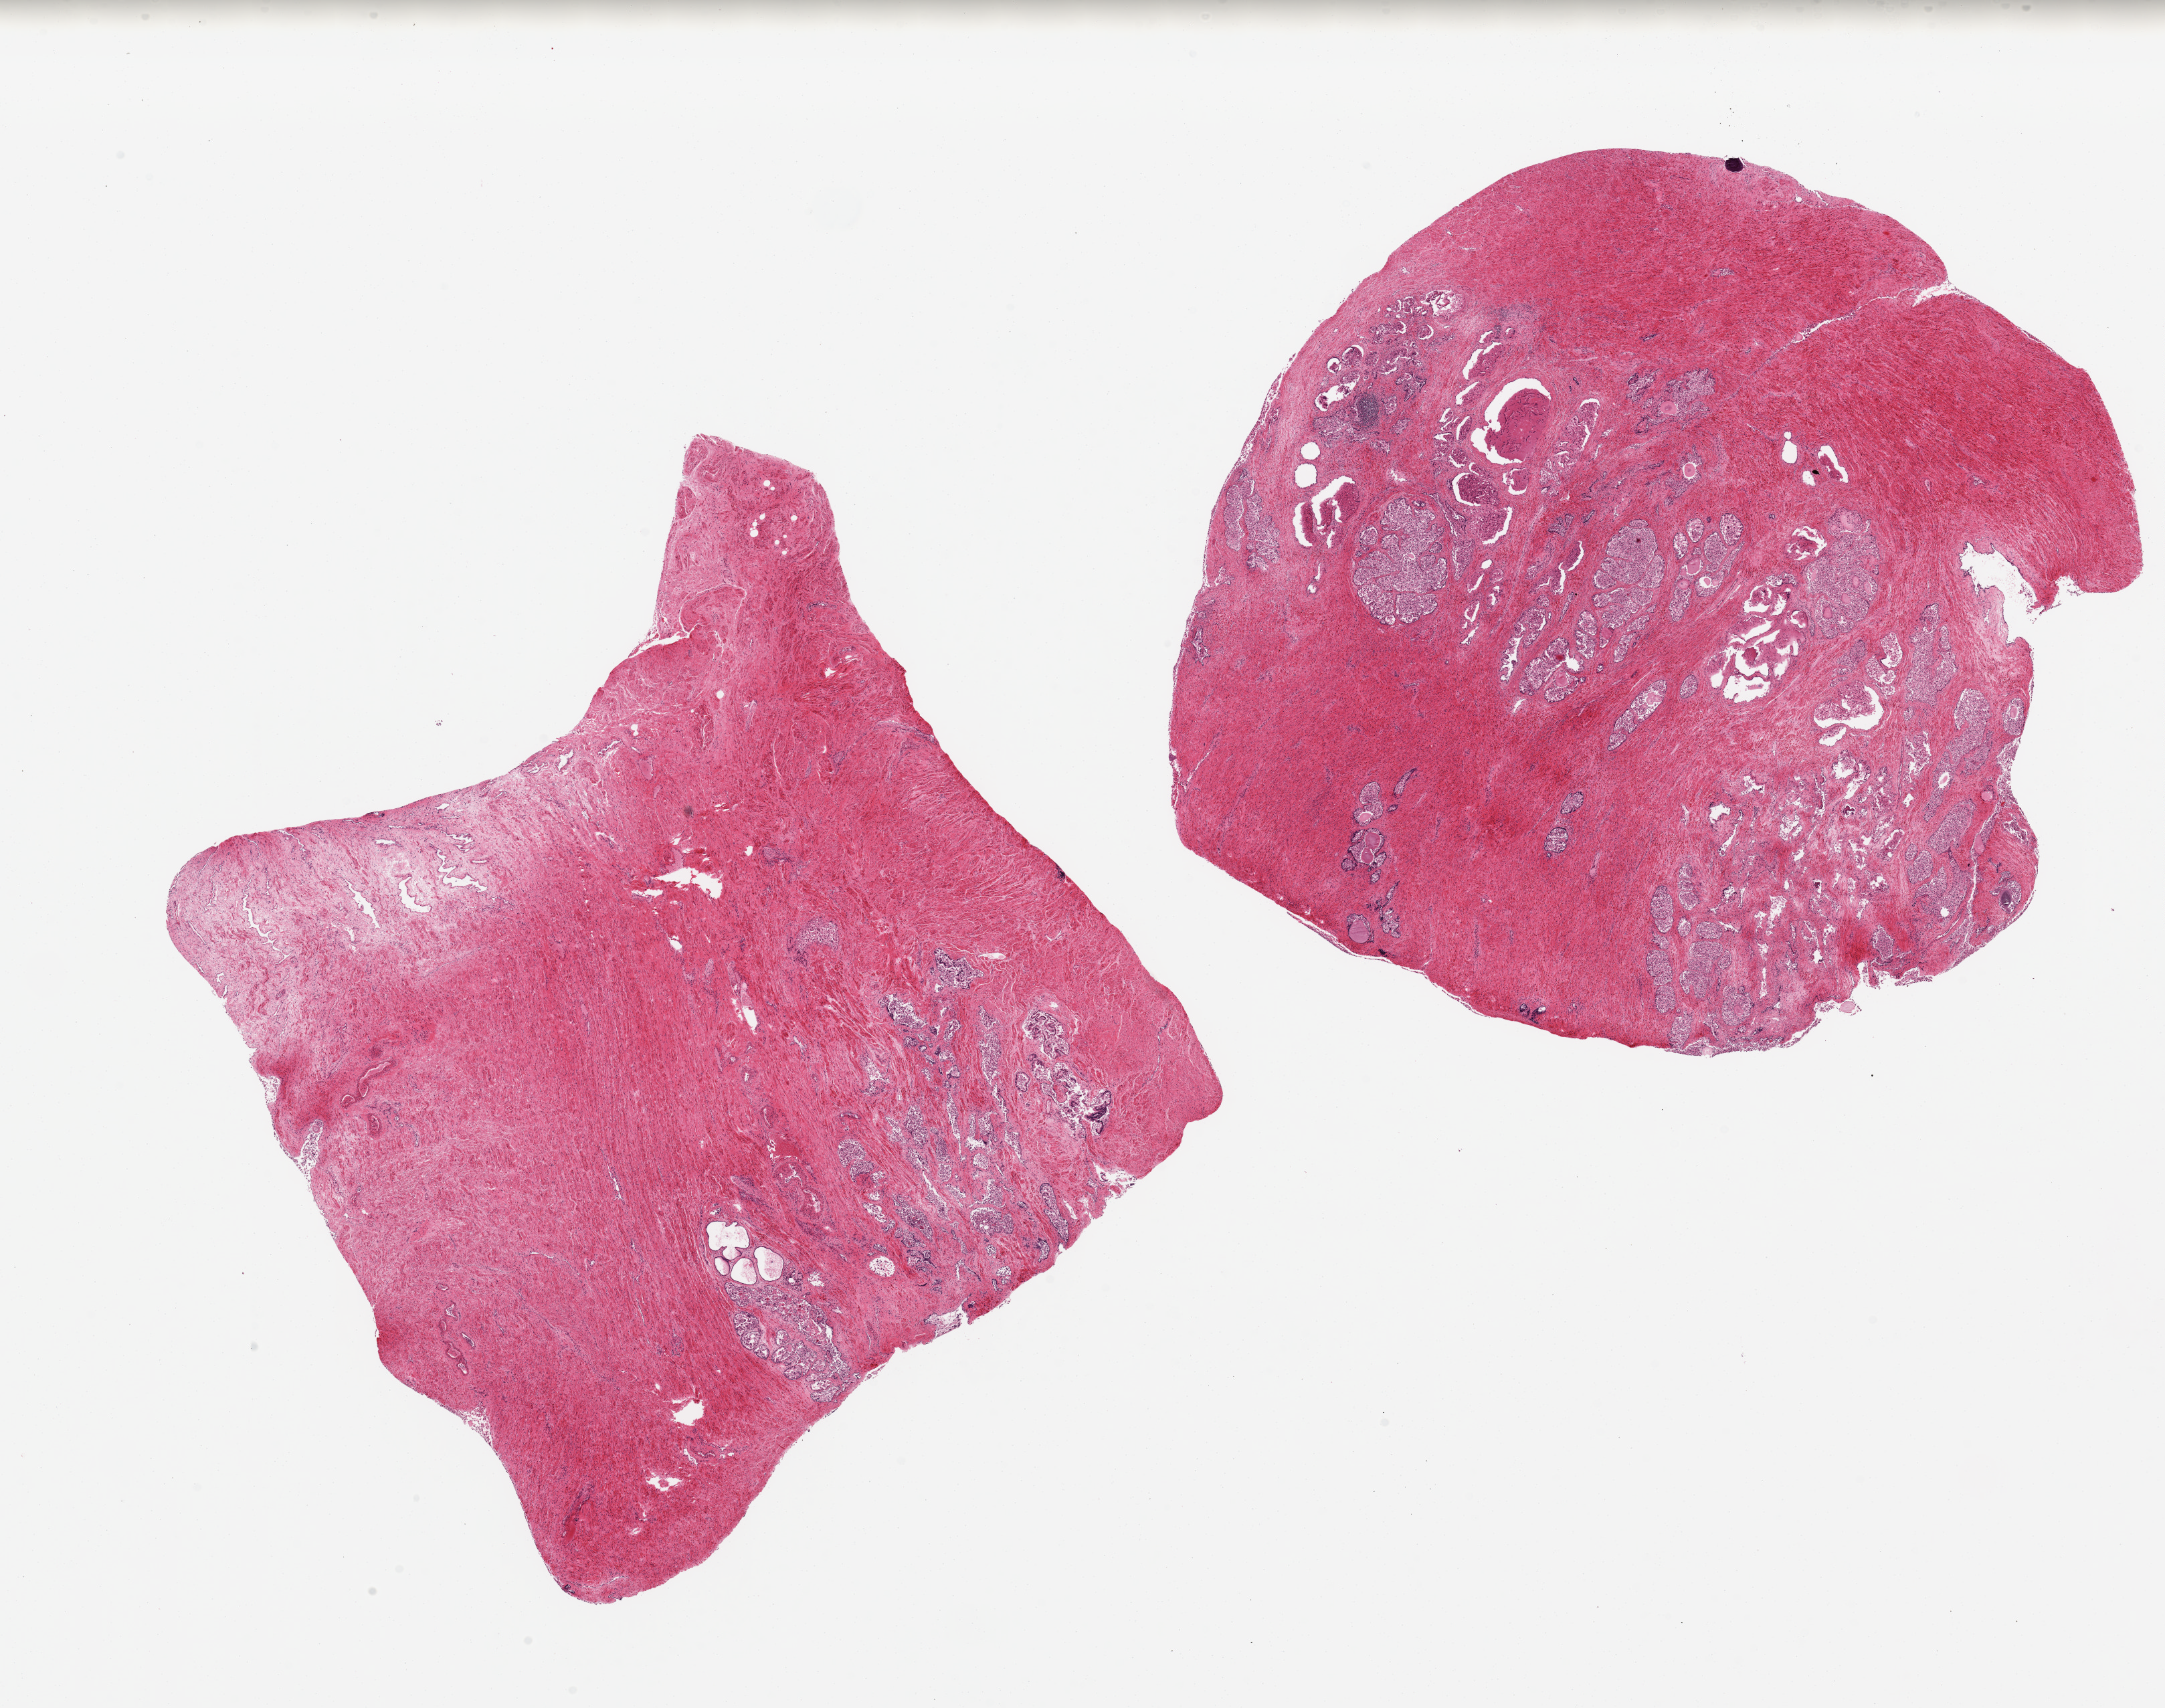
H&E whole-slide image, brightfield, whole scanned area (about 25.6 x 20.2 mm, acquisition: 20x scan) shown as a low-resolution overview. PAXgene-fixed paraffin-embedded (PFPE) section. Section of prostate (target tissue). Donor tissue sample. Donor sex: male.
Pathologist's review note for this sample: 2 pieces, 10x10 mm; severe glandular autolysis, slight stromal autolysis.